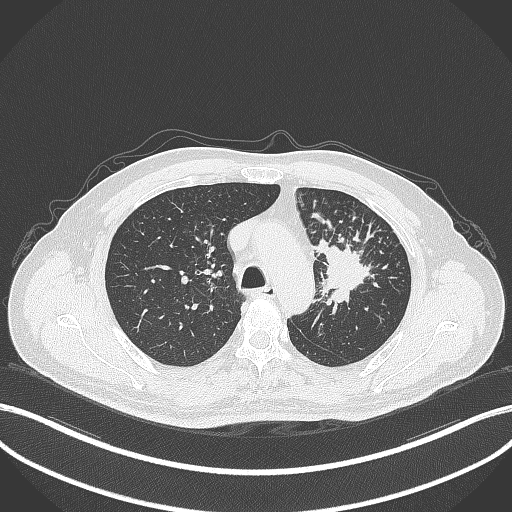
Chest CT, one axial slice; position 259 of 386 along the scan axis; lung window (W 1500 / L -600 HU); 1 mm slice thickness; 512 × 512 image matrix, field of view 400 × 400 mm. Patient: male, 69 years. Case-level facts recorded for this patient, not image findings: clinical TNM (as recorded): T2a N2 M0; histopathological grade: G2-3.
Structures marked on this image (rectangle marked by the reading radiologist):
- lung tumour (recorded histology: adenocarcinoma): bounding box <316,237,373,314> (left, top, right, bottom; pixels)